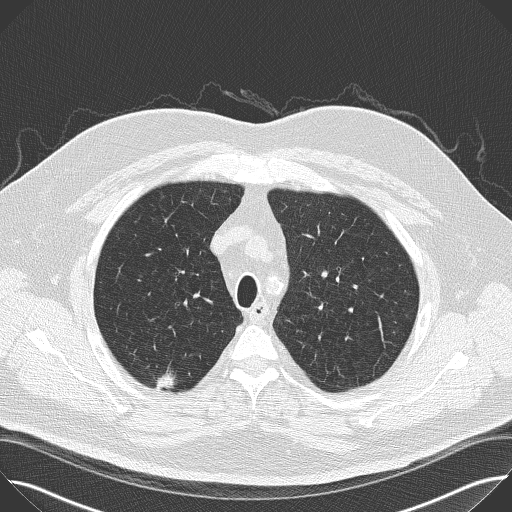
Low-dose screening chest CT, one axial slice; slice 126 of 160 in the series (ordered by position); reconstruction kernel B50f; lung window (W 1500 / L -600 HU); 2 mm slice thickness; 512 × 512 image matrix, field of view 380 × 380 mm.
Outlined on this slice (expert manual segmentation):
- lesion 1 (tumor, upper lobe of right lung): bounding box (x1, y1, x2, y2) in pixels: (156, 369, 175, 392)